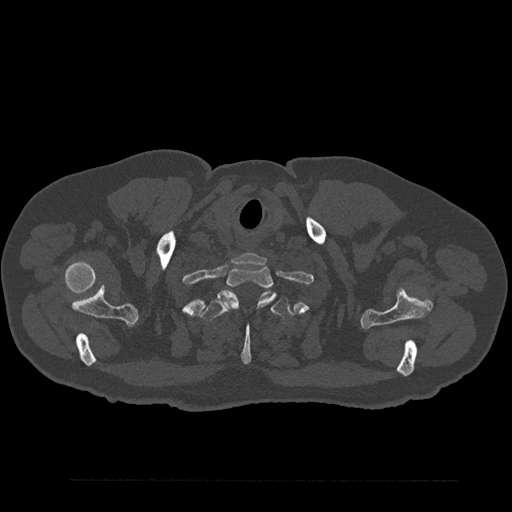
CT including the spine, one axial slice. Position 740 of 797 along the scan axis. Reconstruction kernel Br40s/3. 120 kVp. Bone window (W 1800 / L 400 HU). 0.5 mm slice thickness. 512 × 512 image matrix, field of view 430 × 430 mm. Male patient, age 61 years. Case-level facts recorded for this patient, not image findings: primary cancer: prostate.
Outlined on this slice (semi-automatically segmented with operator editing):
- T1 vertebra: bounding box (x1, y1, x2, y2) in pixels: (218, 267, 275, 310)
- T2 vertebra: (200, 291, 295, 365)